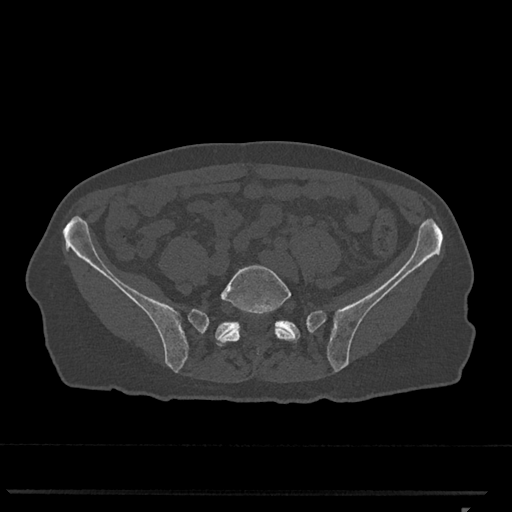
CT including the spine, one axial slice. Position 133 of 793 along the scan axis. Reconstruction kernel Br40s/3. 120 kVp. Bone window (W 1800 / L 400 HU). 0.5 mm slice thickness. 512 × 512 image matrix, field of view 380 × 380 mm. Patient: female, 62 years. From the clinical record (not read from this slice): primary cancer: renal.
Structures marked on this image (semi-automatically segmented with operator editing):
- L5 vertebra: bounding box [x1, y1, x2, y2] px = [217, 265, 297, 354]